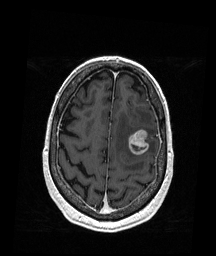
Brain MRI from a brain-tumour surgery series, one axial slice. Slice 50 of 176 in the series (ordered by position). T1-weighted post-contrast. 216 × 256 image matrix, field of view 211 × 250 mm. Case-level facts recorded for this patient, not image findings: histopathology: Metastatic Melanoma; tumour location: Left Frontal.
Annotated regions visible in this slice (expert manual segmentation):
- tumour: box from (x=128, y=129) to (x=149, y=155) px